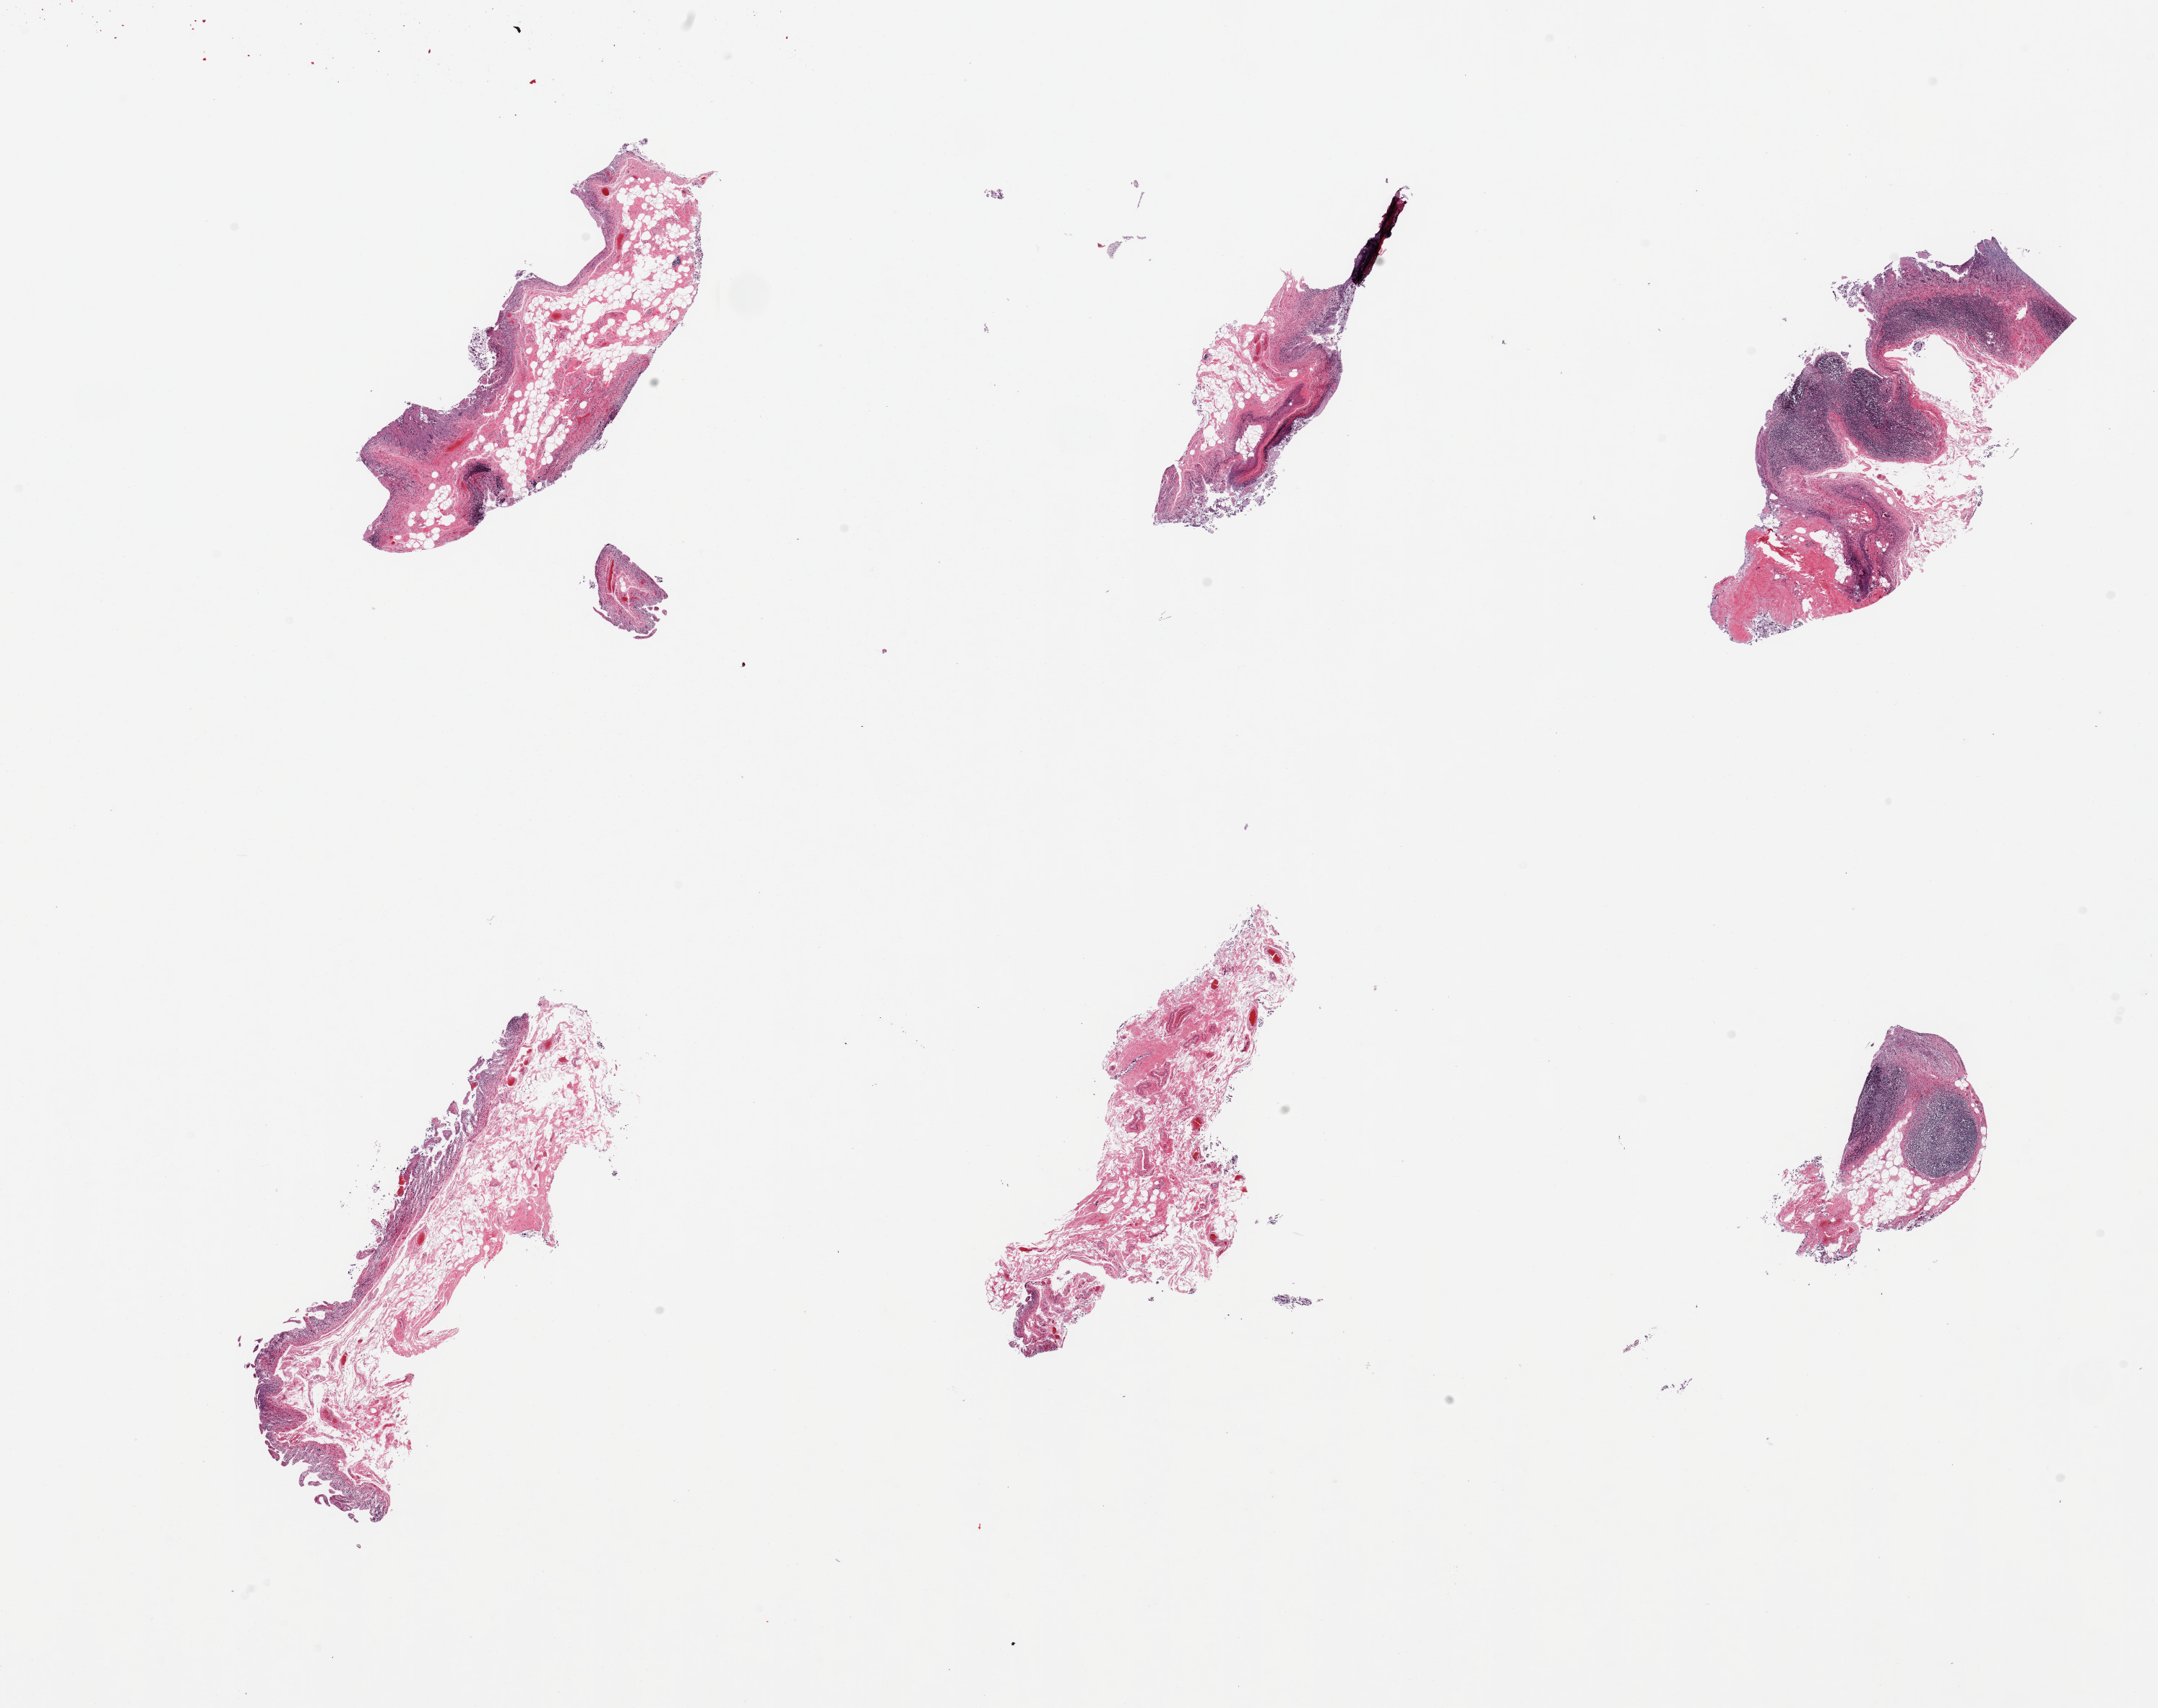
Whole-slide image, H&E stain — a low-resolution overview of the entire scanned area, about 23.6 x 18.7 mm; PAXgene-fixed paraffin-embedded (PFPE) section; section of ileum (target tissue); tissue donor sample. Male donor.
- review note (as recorded): 6 pieces, ~20-30% lymphoid aggregates